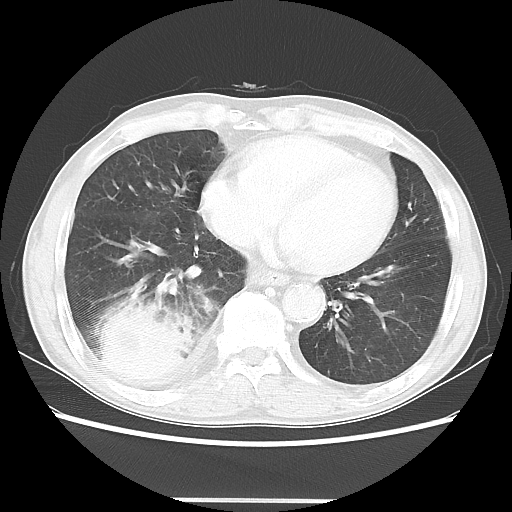
Chest CT, one axial slice; slice 14 of 48 in the series (ordered by position); lung window (W 1500 / L -600 HU); 512 × 512 image matrix, field of view 361 × 361 mm. Patient: male, 66 years. Case-level facts recorded for this patient, not image findings: clinical TNM (as recorded): T4 N1 M1; histopathological grade: G3.
Structures marked on this image (bounding box drawn by a radiologist):
- lung tumour (recorded histology: small cell carcinoma): bounding box <85,292,198,409> (left, top, right, bottom; pixels)